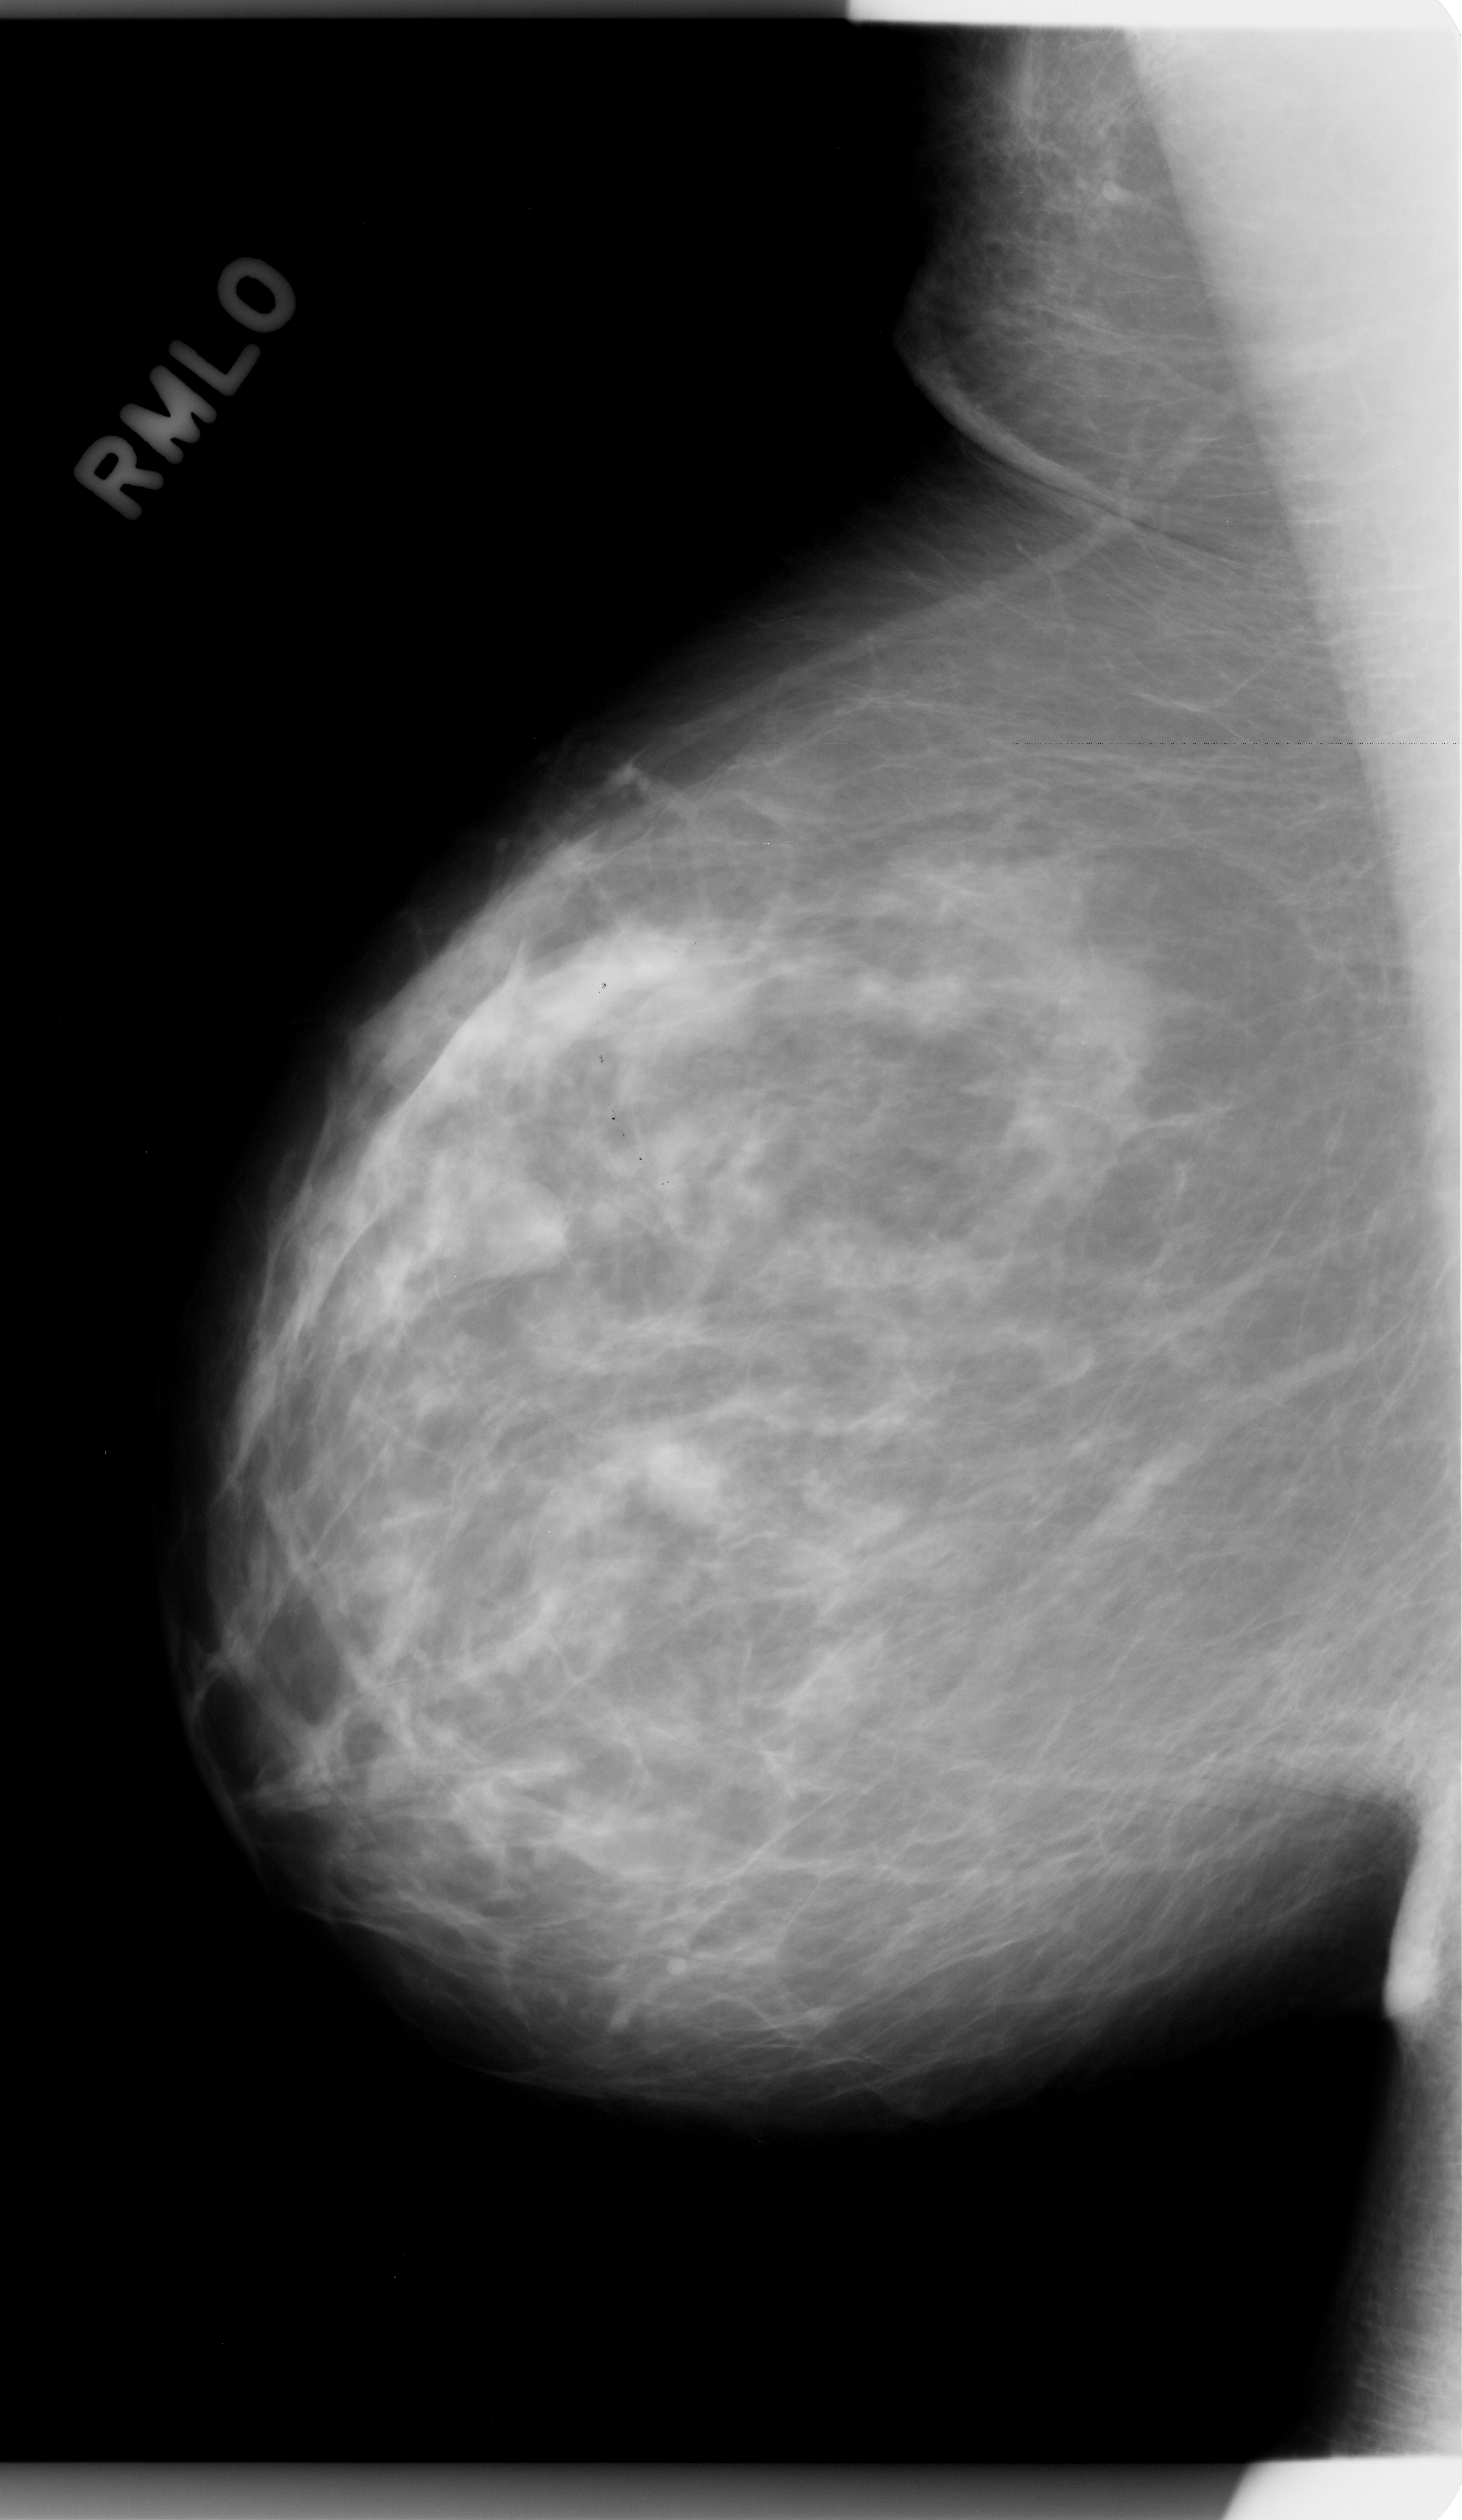
Digitized screen-film mammogram; right breast; mediolateral oblique (MLO) view; breast composition: scattered fibroglandular densities (BI-RADS density category 2 of 4); 1462 × 2520 image matrix.
Expert-marked regions of interest on this image (one box per marked abnormality):
- mass, shape round, margins obscured; BI-RADS assessment category 3; pathology (as recorded): benign: bounding box <454,1163,573,1280> (left, top, right, bottom; pixels)